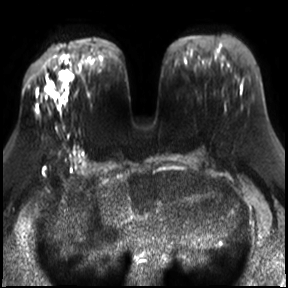
Breast MRI, one axial slice; position 11 of 30 along the scan axis; diffusion-weighted series; image 2 of 4 stored at this slice position (different b-values; order by instance number); 3 T; 288 × 288 image matrix. Female patient.
Annotated regions visible in this slice (manually delineated by an expert):
- tumour on diffusion-weighted imaging: bounding box [x1, y1, x2, y2] px = [48, 86, 52, 92]